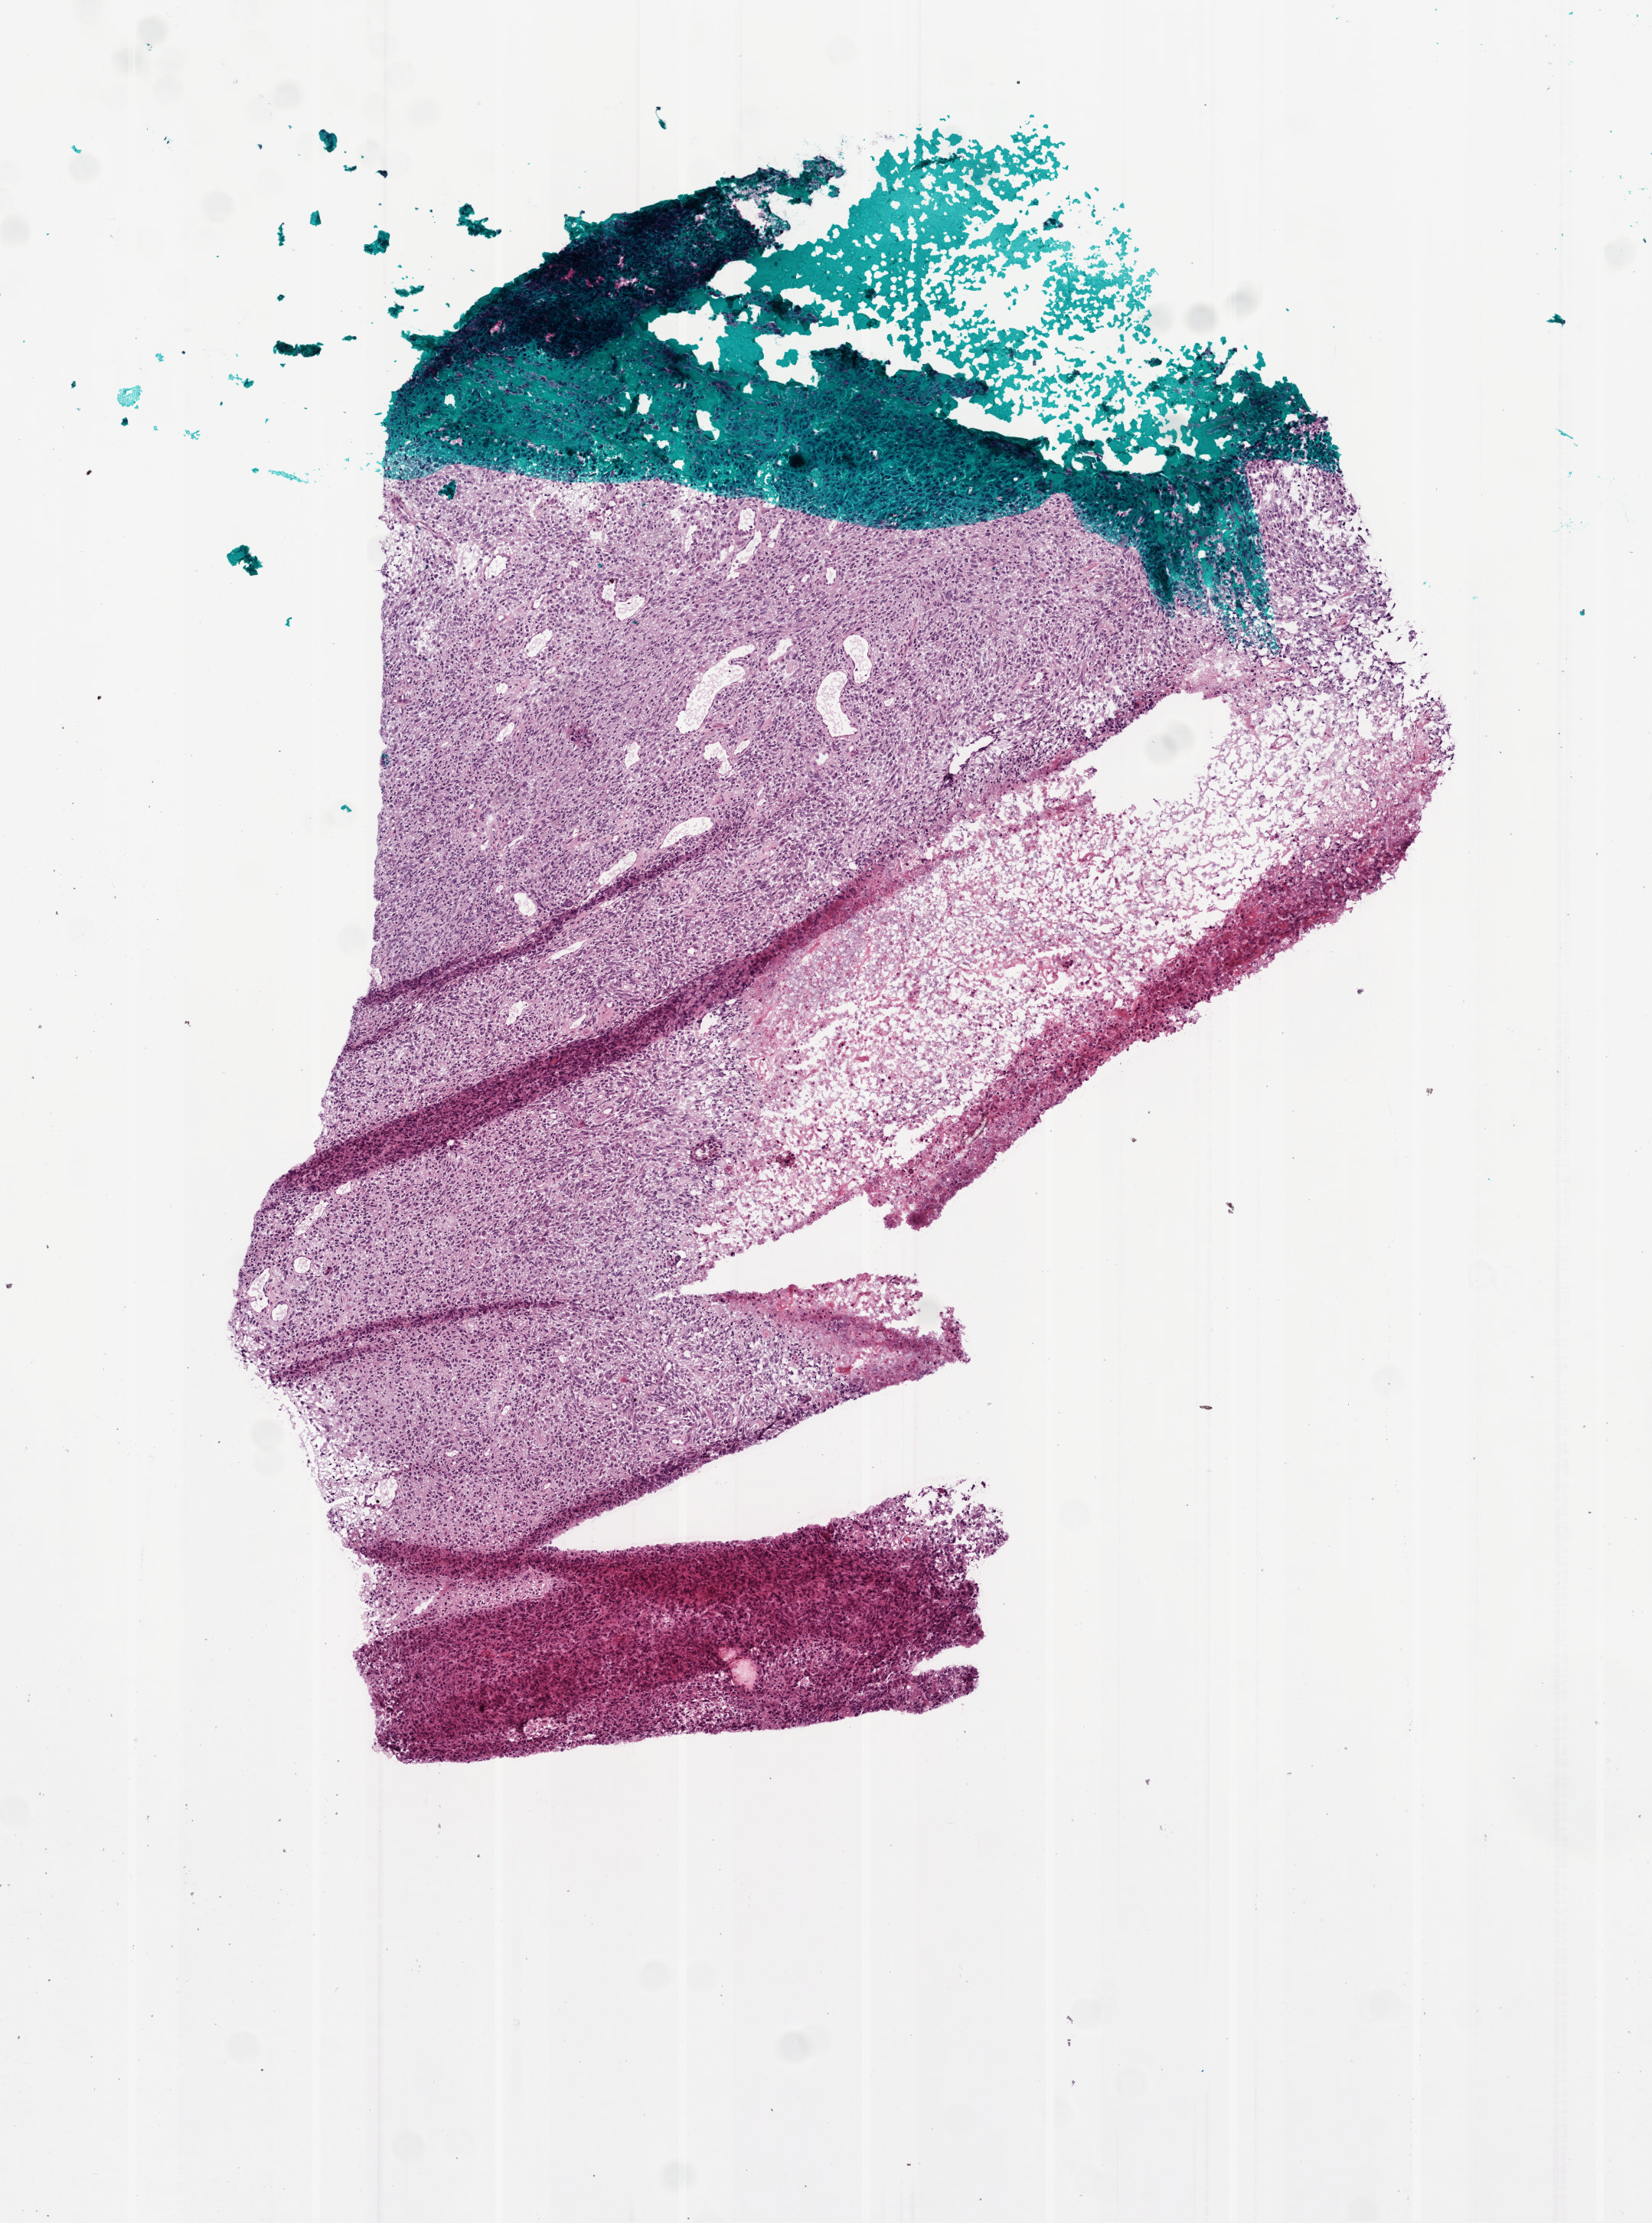
Digitized Hematoxylin and eosin (H&E) stained tissue section (whole slide), whole scanned area (about 4.4 x 5.9 mm, from a 20x scan) shown as a low-resolution overview, frozen section from the bottom of the tissue portion, sample: primary tumour, brain. Male patient; age at initial diagnosis 75 years. Composition of this section per pathologist review: tumour cells 80%, tumour nuclei 100%, normal cells 0%, stromal cells 0%, necrosis 20%.
- histologic diagnosis: Glioblastoma